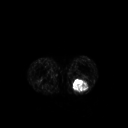
FDG PET of an extremity soft-tissue mass (from a PET/CT study), one axial slice; slice 191 of 267 in the series (ordered by position); 3.27 mm slice thickness; 128 × 128 image matrix, field of view 500 × 500 mm. Male patient, age 54 years. From the clinical record (not read from this slice): histological type: synovial sarcoma; site of the primary tumour: left poplietal fossa.
Outlined on this slice (expert contour drawn on MRI and transferred to this co-registered scan by the dataset authors):
- gross tumour volume (mass): bounding box <72,78,90,93> (left, top, right, bottom; pixels)